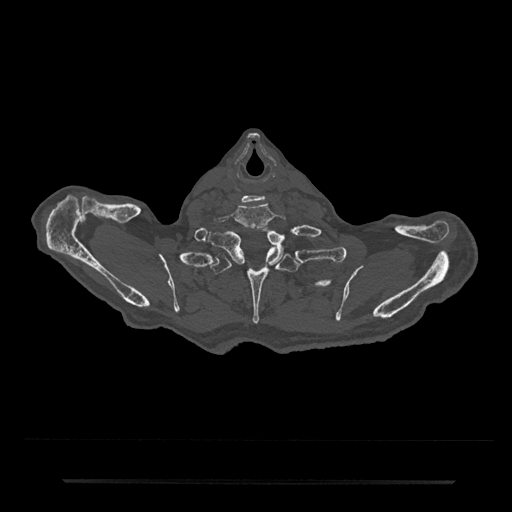
CT including the spine, one axial slice. Slice 712 of 797 in the series (ordered by position). Reconstruction kernel Br40s/3. Bone window (W 1800 / L 400 HU). 0.5 mm slice thickness. 512 × 512 image matrix, field of view 427 × 427 mm. Male patient, age 74 years. Case-level facts recorded for this patient, not image findings: primary cancer: prostate.
Structures marked on this image (semi-automatic segmentation, software-assisted and operator-edited):
- T1 vertebra: box from (x=209, y=226) to (x=284, y=267) px
- T2 vertebra: (x=210, y=248)–(x=305, y=324)